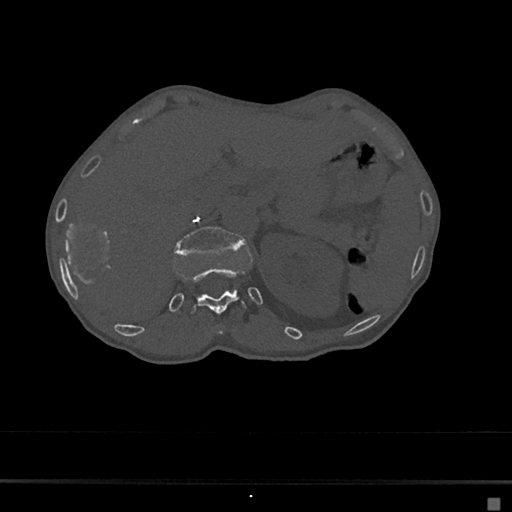
CT including the spine, one axial slice; position 115 of 797 along the scan axis; 120 kVp; bone window (W 1800 / L 400 HU); 512 × 512 image matrix, field of view 360 × 360 mm. Patient: female, 68 years. Case-level facts recorded for this patient, not image findings: primary cancer: renal.
Outlined on this slice (semi-automatically segmented with operator editing):
- L1 vertebra: bounding box [x1, y1, x2, y2] px = [173, 226, 246, 256]
- T11 vertebra: [216, 331, 223, 336]
- T12 vertebra: [188, 267, 247, 315]